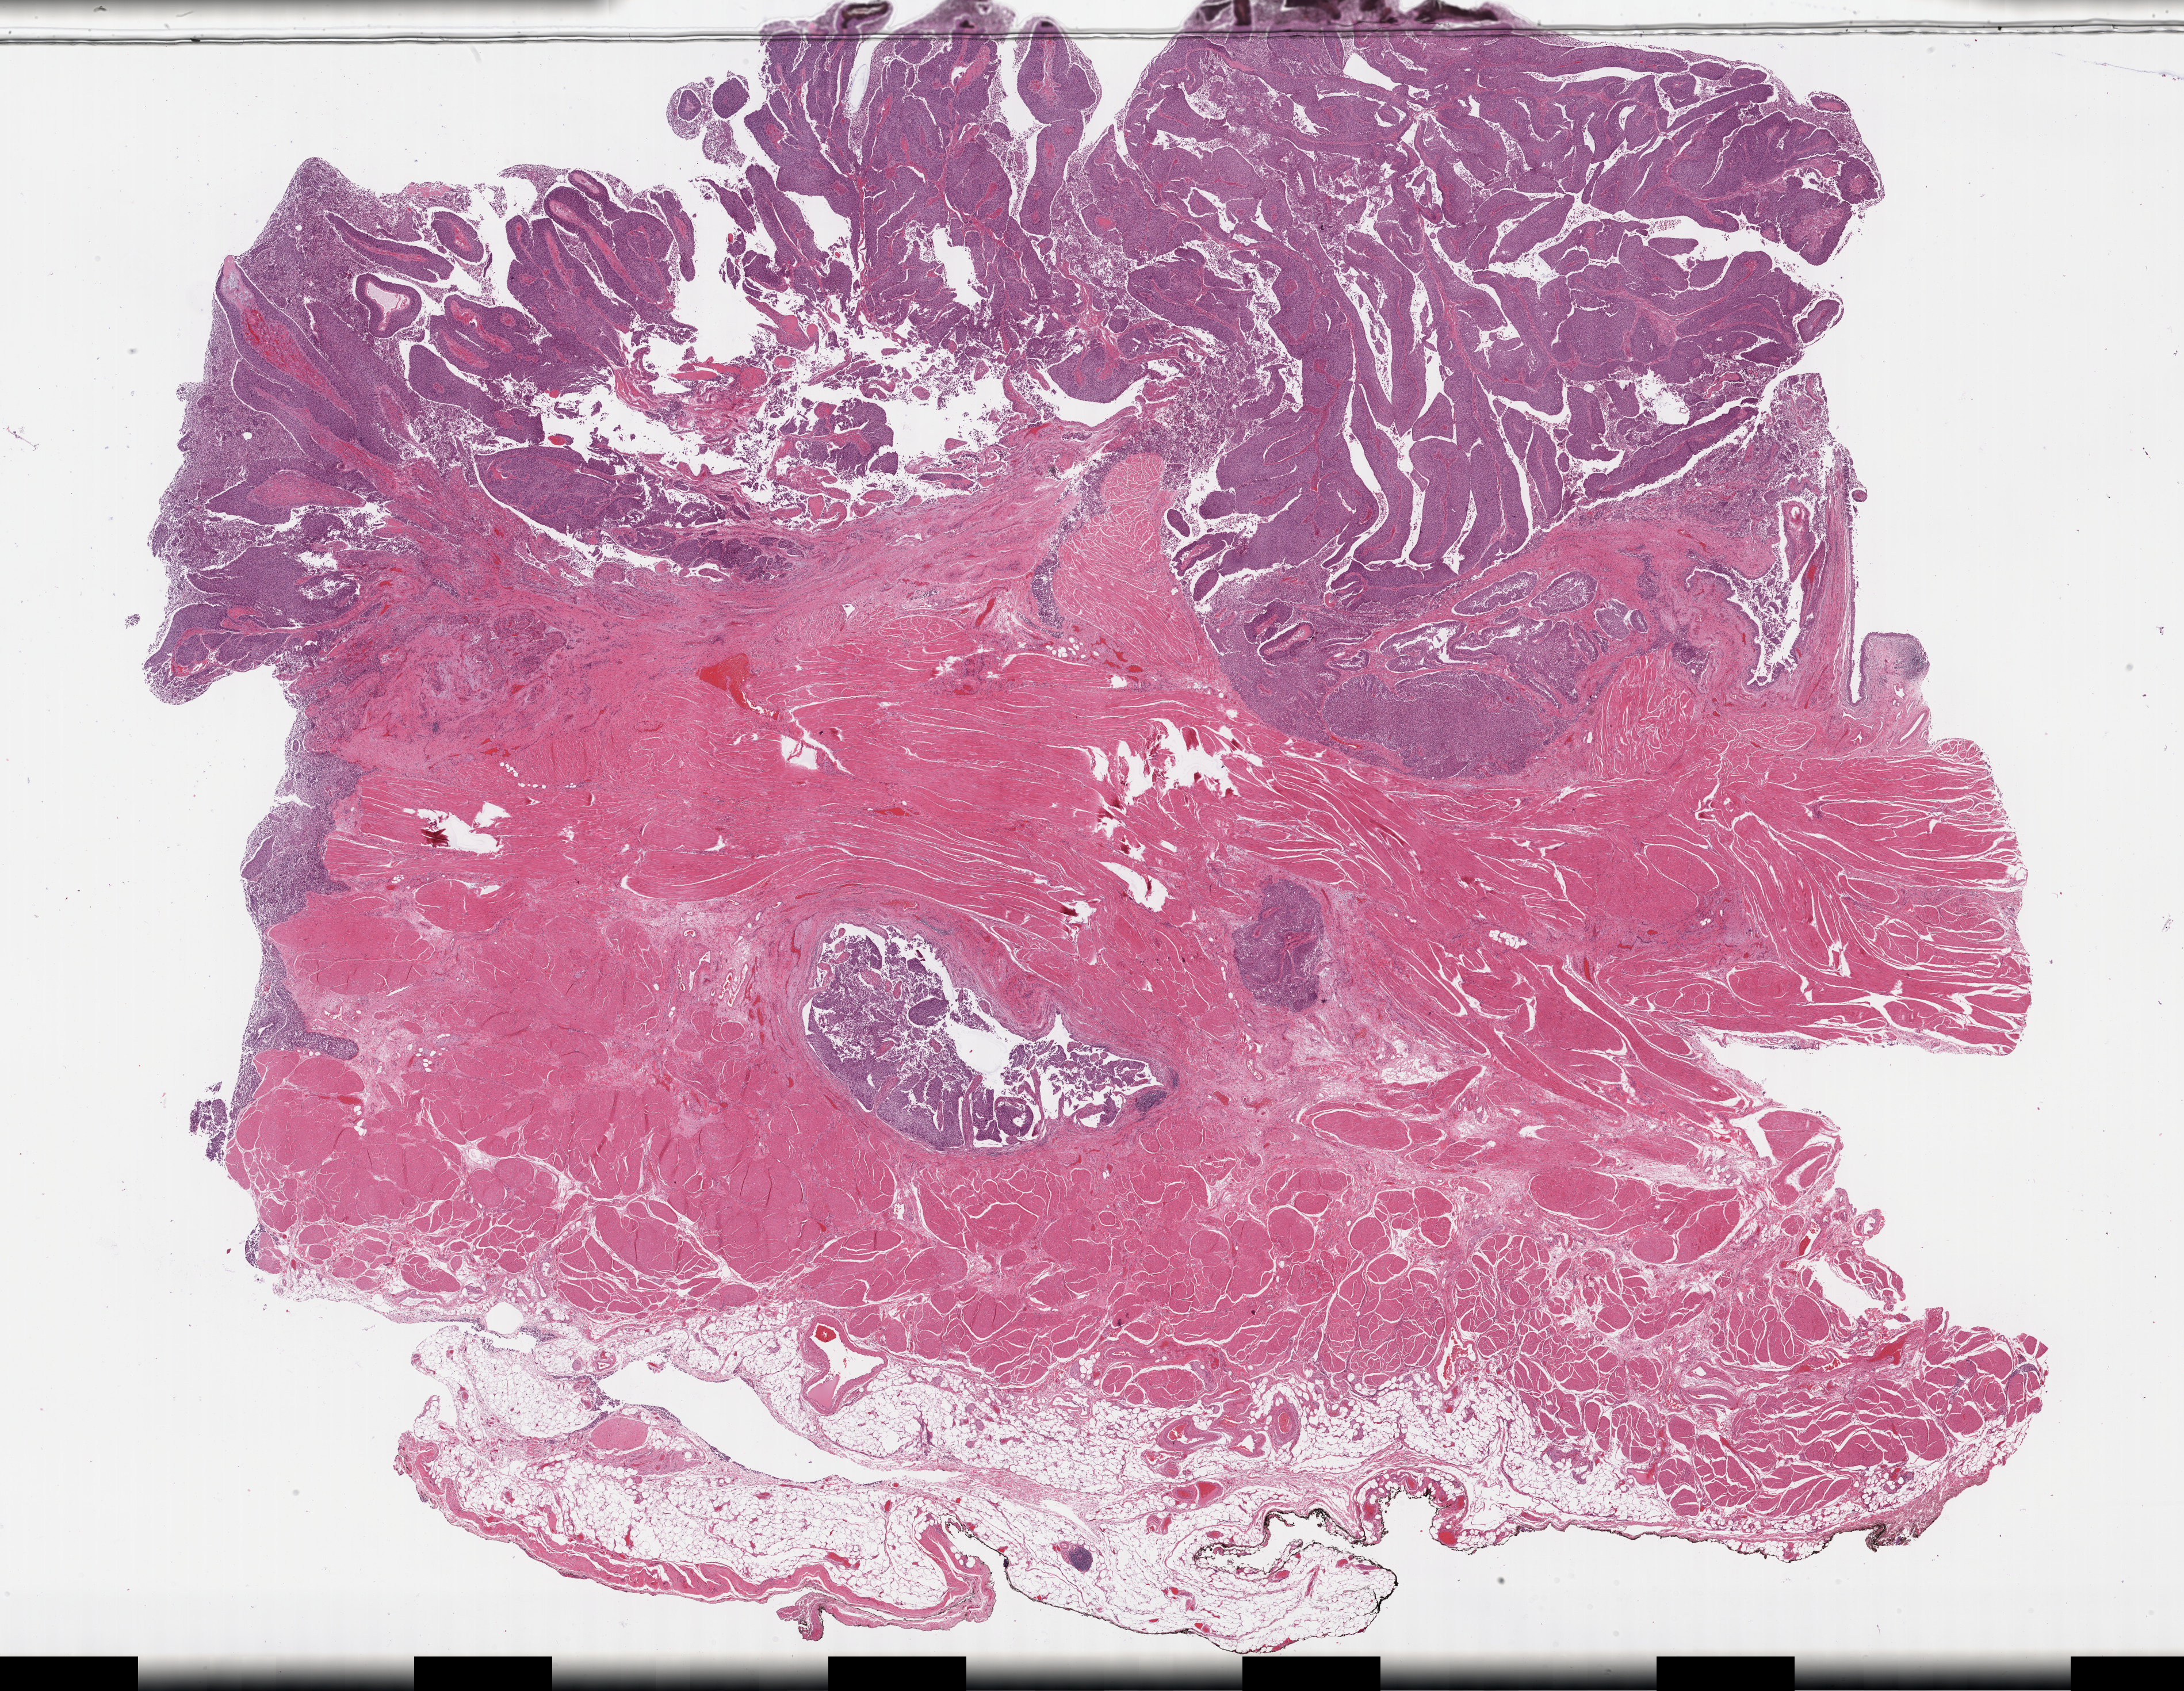
H&E whole-slide image, low-resolution overview of the scanned area, about 30.7 x 23.8 mm (slide scanned at 40x). Formalin-fixed paraffin-embedded (FFPE) diagnostic section. Sample: primary tumour, bladder. Male patient; age at initial diagnosis 84 years. Histologic grade: high grade.
Lymph nodes positive (case pathology): 0 of 28 examined. Diagnosis: Papillary transitional cell carcinoma (posterior wall of bladder). TNM: T2a N0 MX. AJCC pathologic stage: II (7th edition).